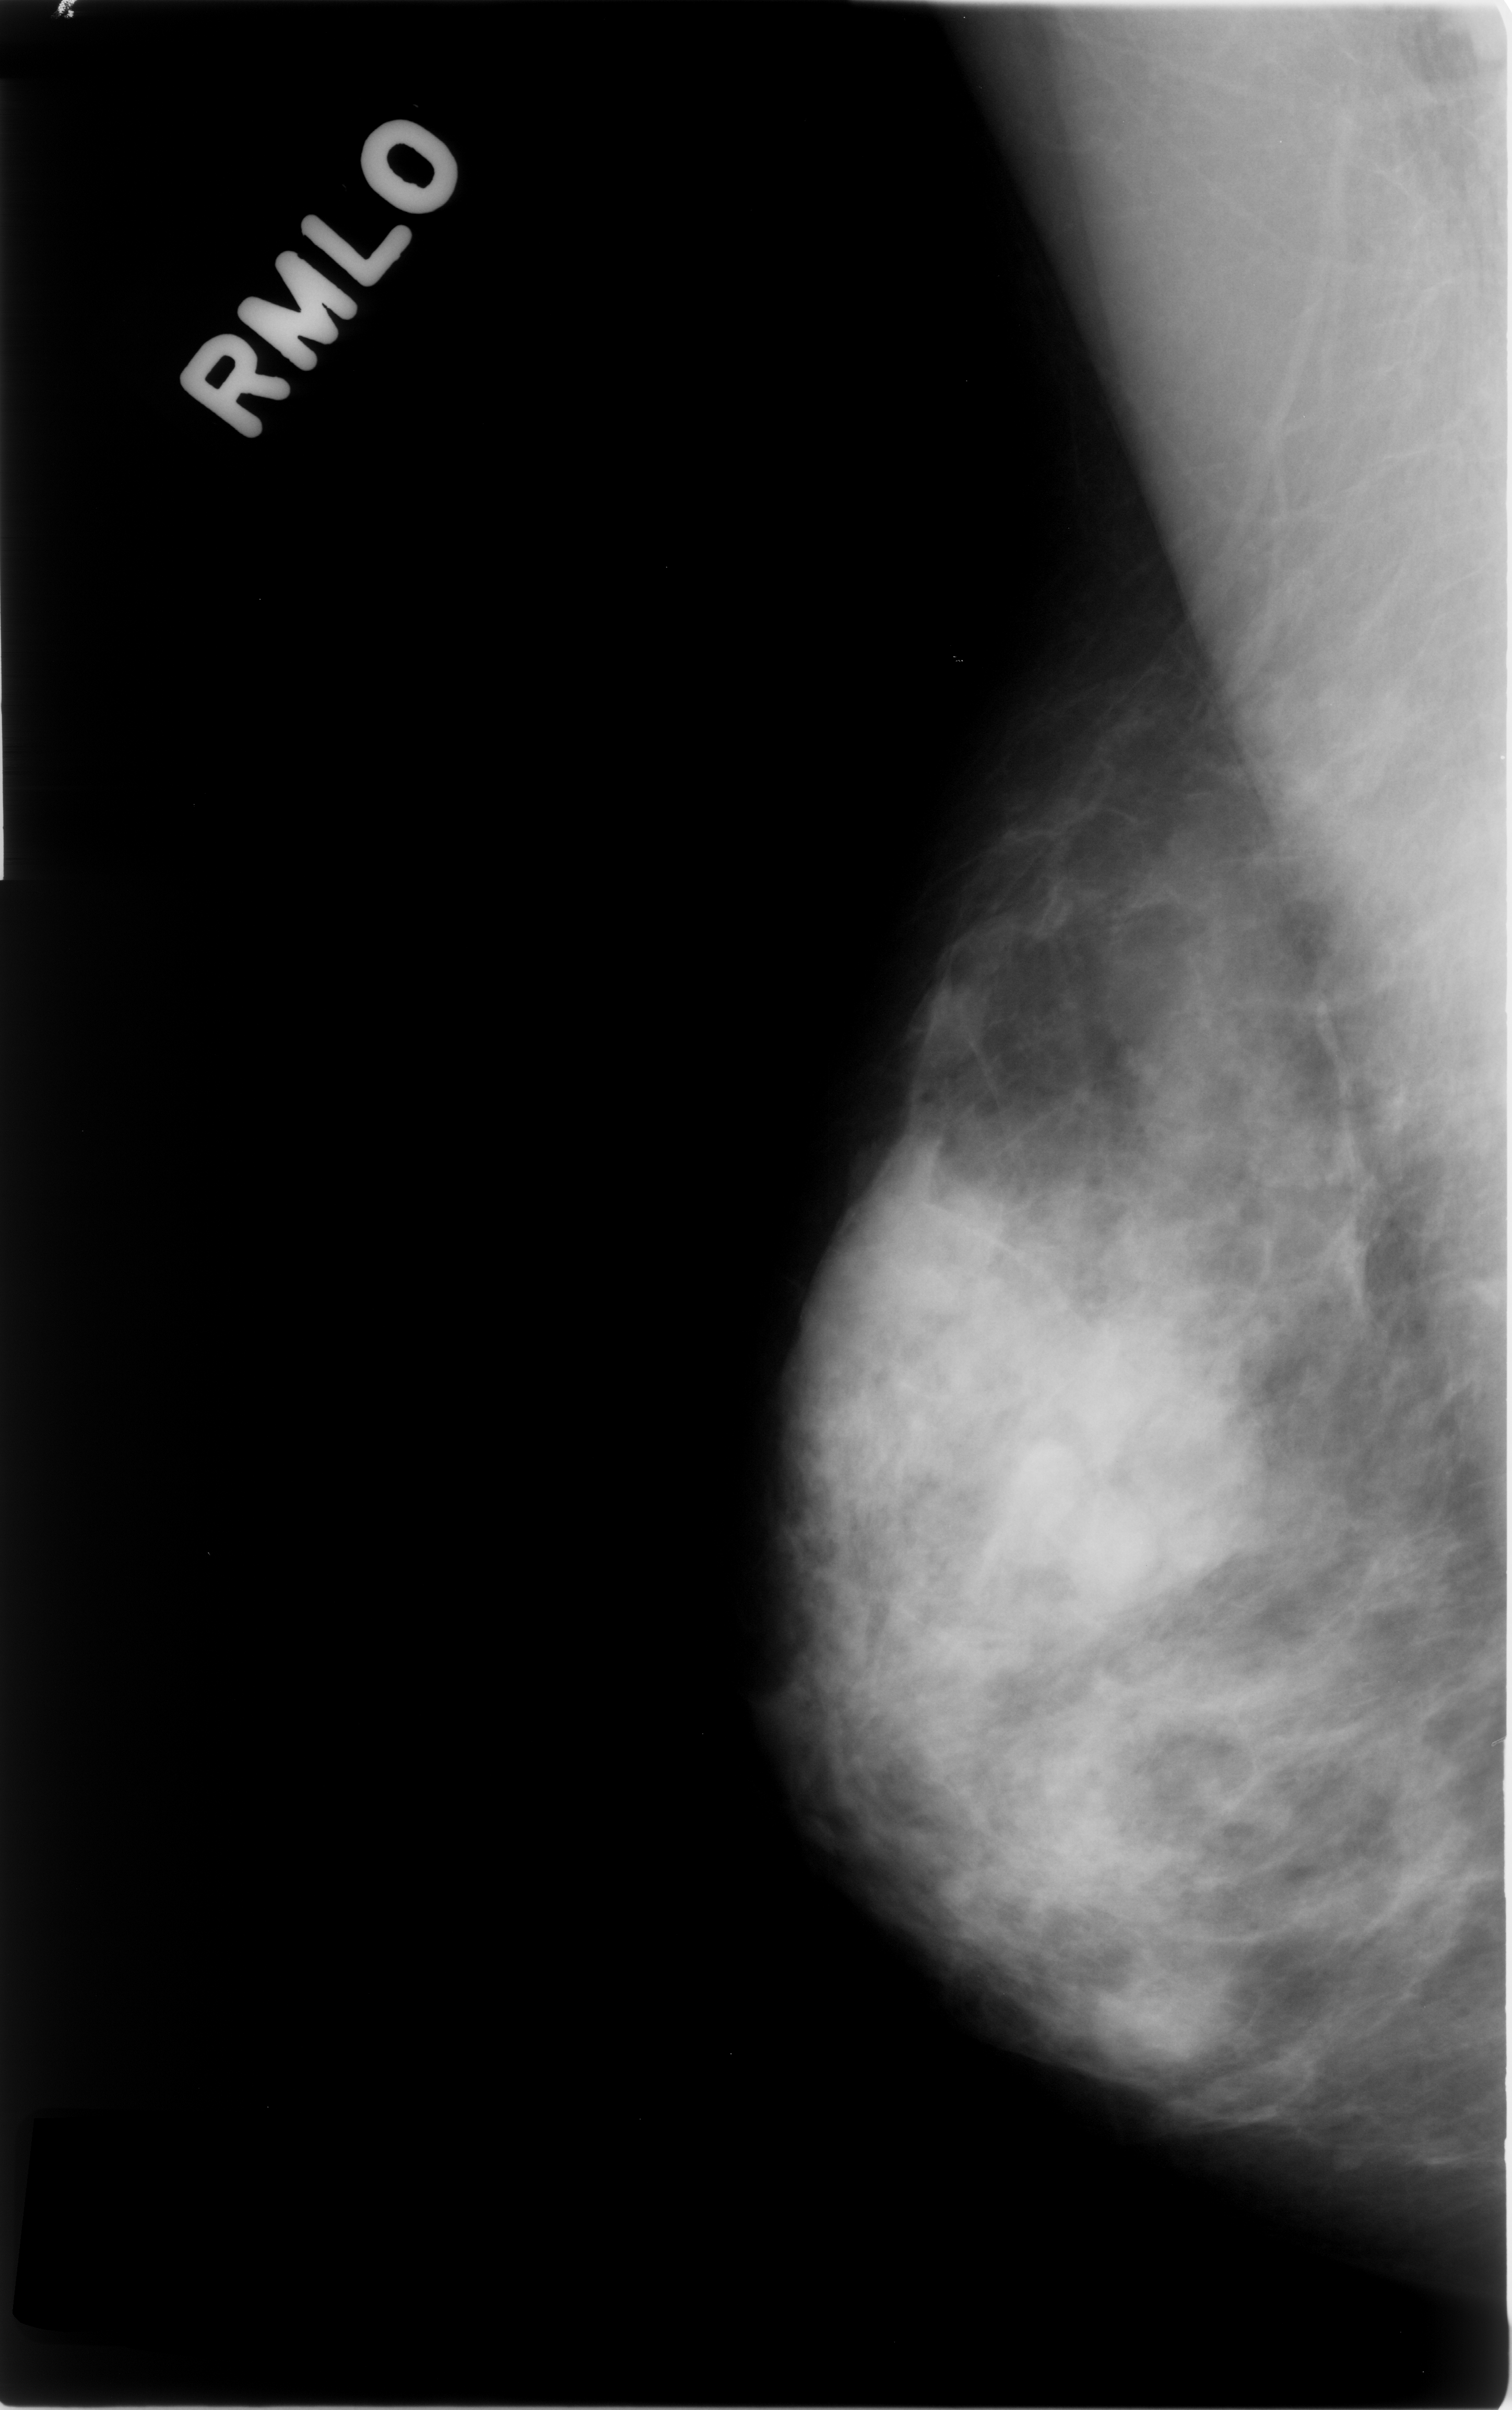
Digitized screen-film mammogram. Right breast. Mediolateral oblique (MLO) view. Breast composition: heterogeneously dense (BI-RADS density category 3 of 4). 1512 × 2410 image matrix.
Expert-marked regions of interest on this film, with their recorded descriptors:
- mass, shape lobulated, margins obscured; BI-RADS assessment category 3; pathology result (as recorded, not read from the image): benign: bounding box [x1, y1, x2, y2] px = [1046, 1391, 1237, 1610]